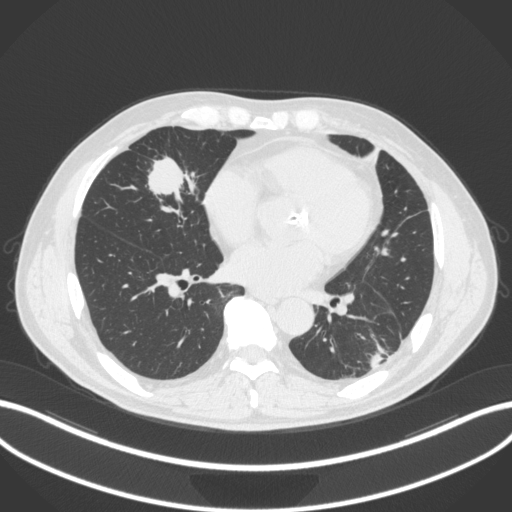
Chest CT, one axial slice. Position 118 of 399 along the scan axis. Reconstruction kernel B31f. 120 kVp. Lung window (W 1500 / L -600 HU). 1 mm slice thickness. 512 × 512 image matrix. Male patient, age 59 years. From the clinical record (not read from this slice): clinical TNM (as recorded): T2a N1 M0.
Annotated regions visible in this slice (rectangle marked by the reading radiologist):
- lung tumour (recorded histology: adenocarcinoma): bounding box [x1, y1, x2, y2] px = [135, 152, 198, 207]